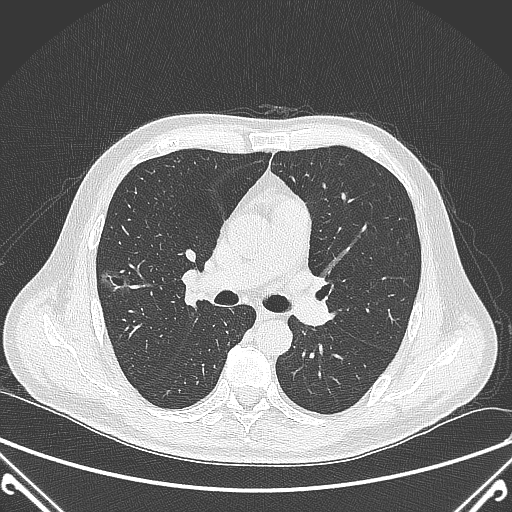
Chest CT, one axial slice. Slice 222 of 360 in the series (ordered by position). 120 kVp. Lung window (W 1500 / L -600 HU). 512 × 512 image matrix, field of view 380 × 380 mm. Patient: male, 64 years. Case-level facts recorded for this patient, not image findings: clinical TNM (as recorded): T1c N0 M0; histopathological grade: G2.
Outlined on this slice (bounding box drawn by a radiologist):
- lung tumour (recorded histology: adenocarcinoma): bounding box [x1, y1, x2, y2] px = [96, 266, 137, 300]